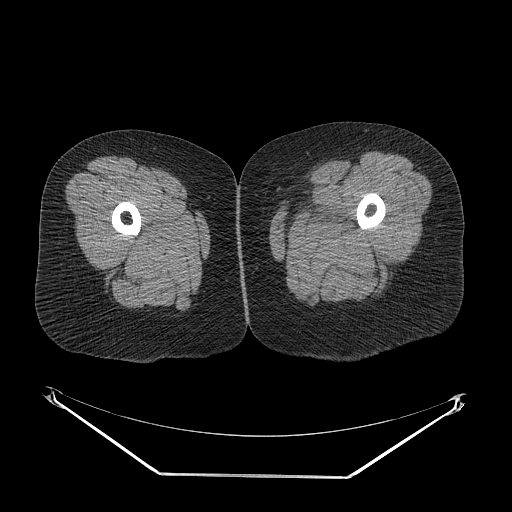
CT of an extremity soft-tissue mass (from a PET/CT study), one axial slice; slice 10 of 267 in the series (ordered by position); soft-tissue window (W 400 / L 40 HU); 3.75 mm slice thickness; 512 × 512 image matrix, field of view 500 × 500 mm. Female patient. From the clinical record (not read from this slice): histological type: myxofibrosarcoma; grade: intermediate; site of the primary tumour: left thigh.
Annotated regions visible in this slice (expert contour drawn on MRI and transferred to this co-registered scan by the dataset authors):
- gross tumour volume including surrounding oedema: bounding box (x1, y1, x2, y2) in pixels: (281, 199, 352, 239)